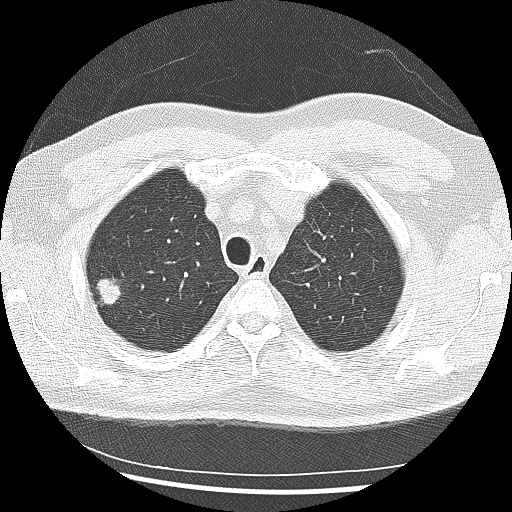
Low-dose screening chest CT, one axial slice. Slice 215 of 265 in the series (ordered by position). 120 kVp. Lung window (W 1500 / L -600 HU). 512 × 512 image matrix, field of view 340 × 340 mm.
Annotated regions visible in this slice (outlined manually by an expert reader):
- lesion 1 (tumor, upper lobe of right lung): box from (x=97, y=278) to (x=121, y=305) px